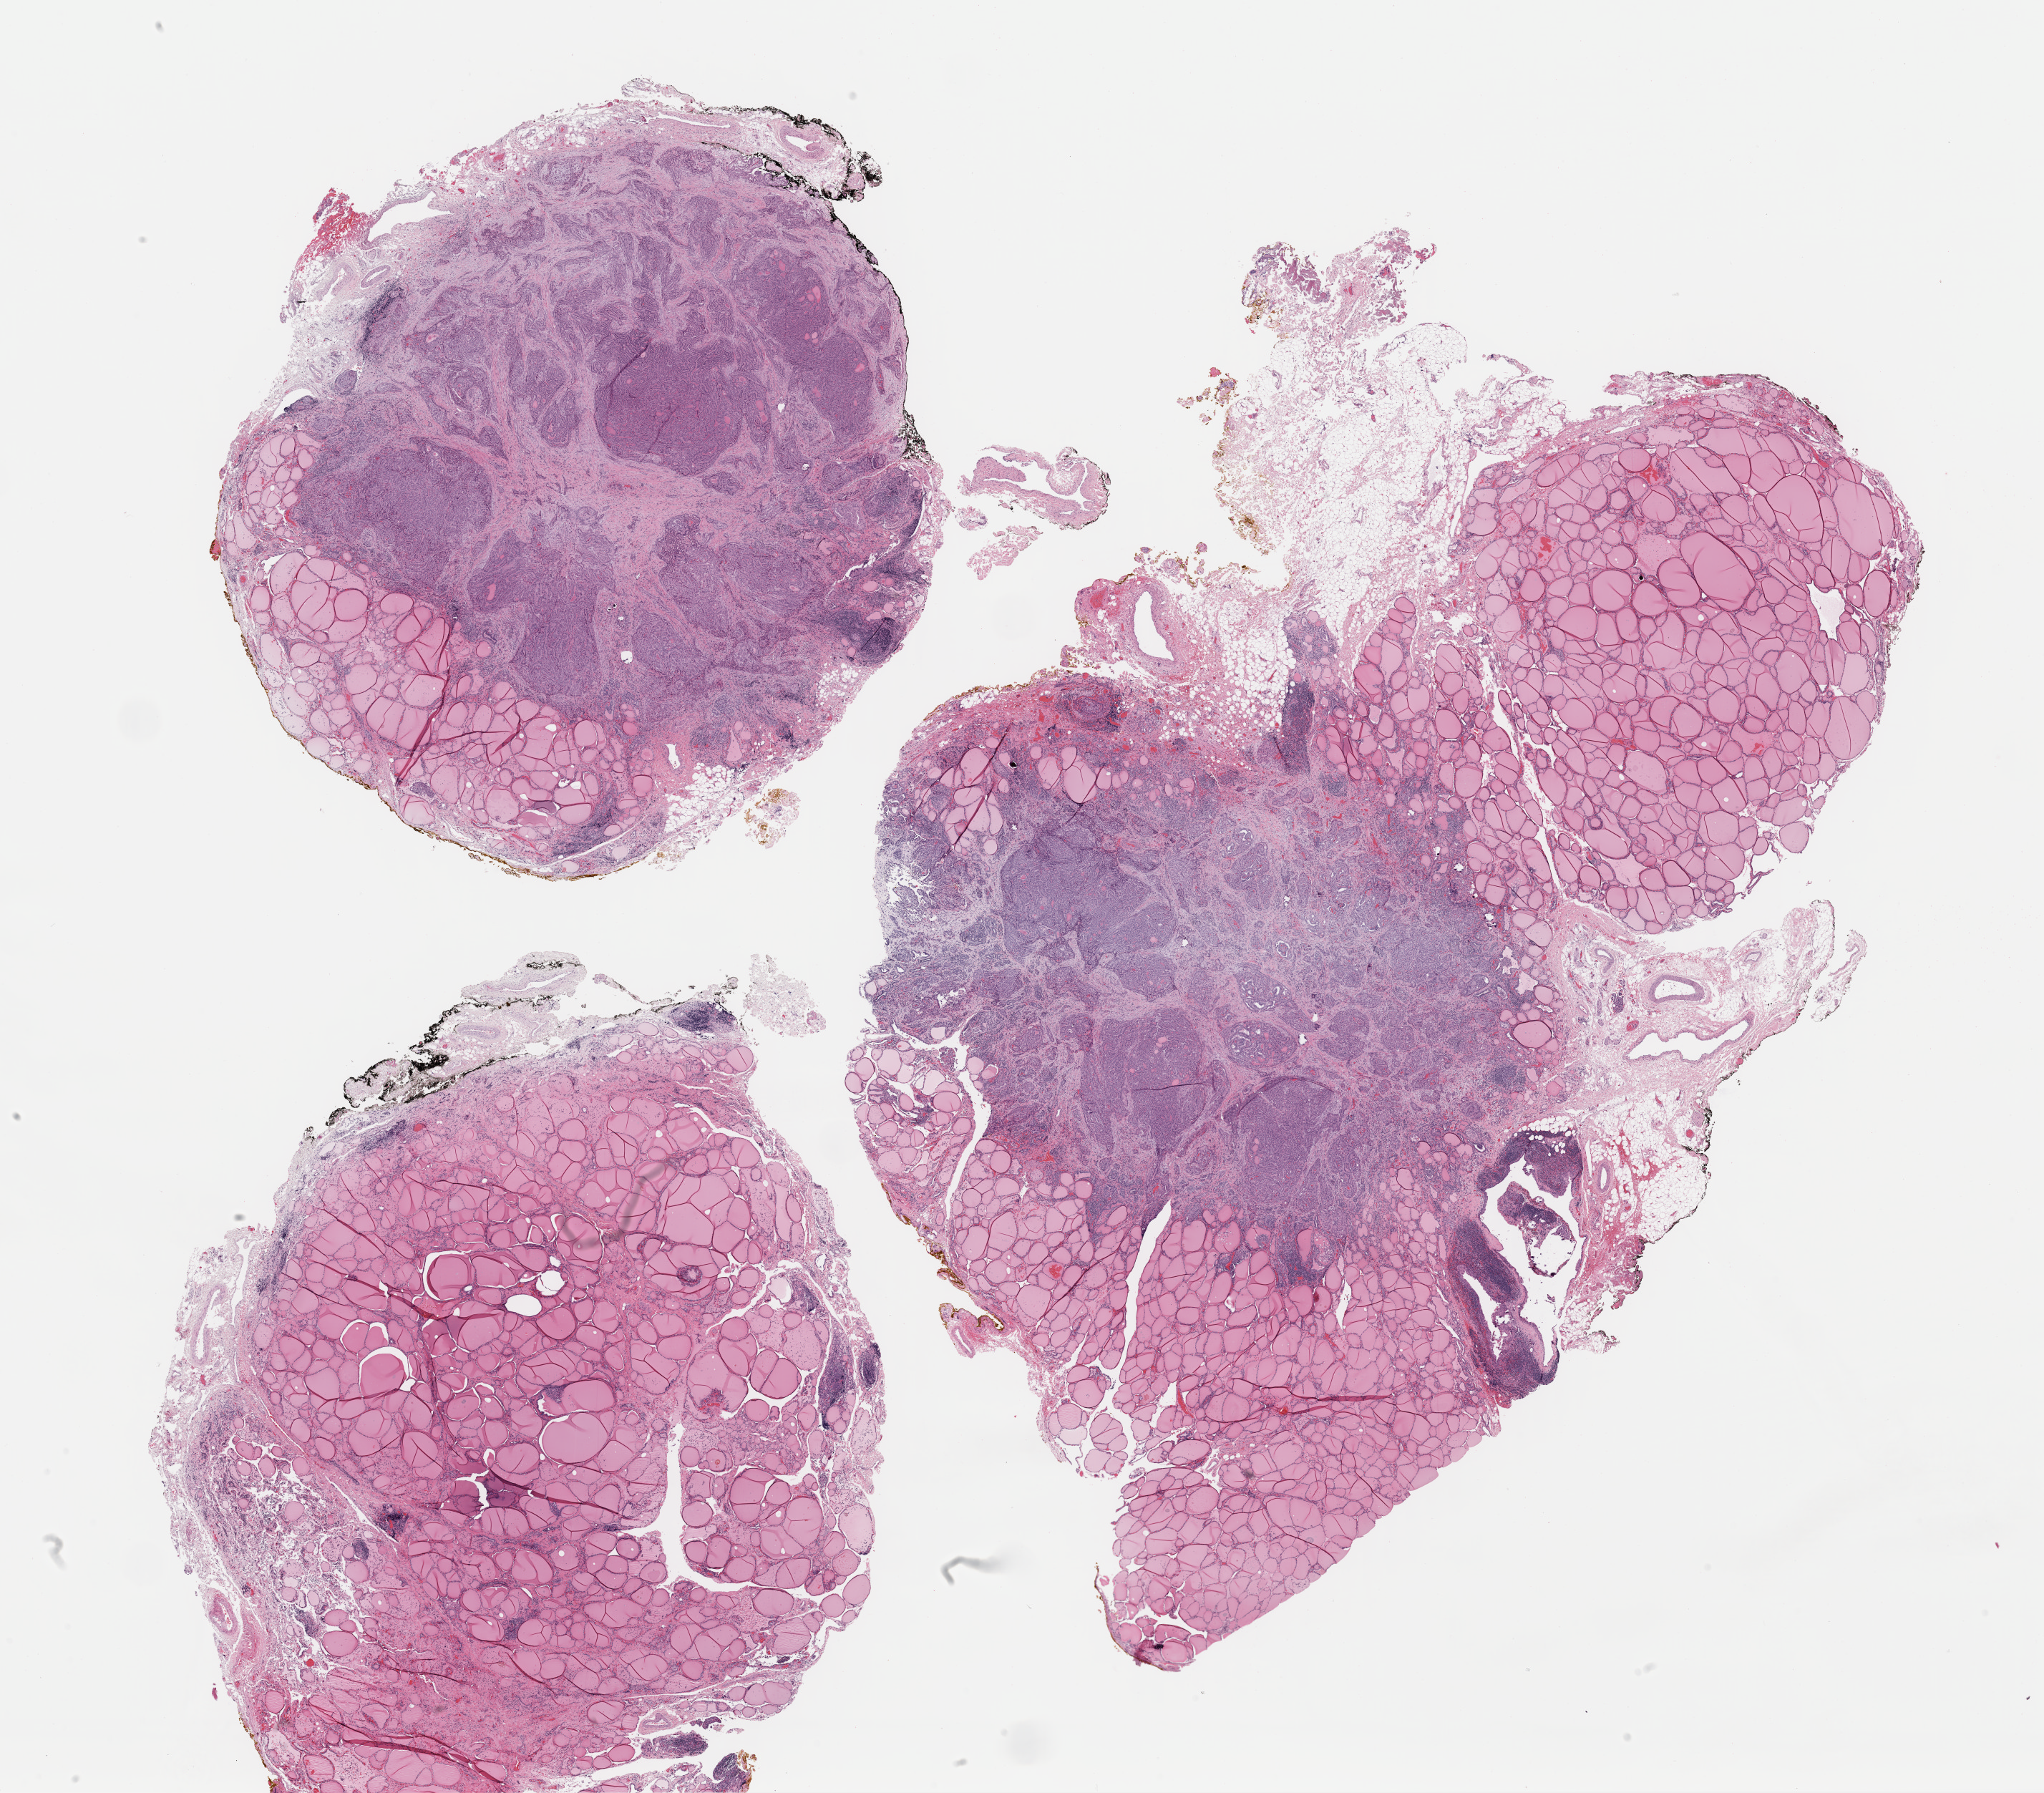
Digitized H&E-stained tissue section (whole slide), a low-resolution overview of the entire scanned area, about 22.6 x 19.8 mm (from a 40x scan); formalin-fixed paraffin-embedded (FFPE) diagnostic section; sample: primary tumour, thyroid. Female, age 33 years at initial diagnosis.
• lymph nodes positive (case pathology): 5 of 5 examined
• histologic diagnosis: Papillary adenocarcinoma, NOS (thyroid gland)
• TNM: T3 N1a MX
• laterality: right
• AJCC pathologic stage: I (6th edition)